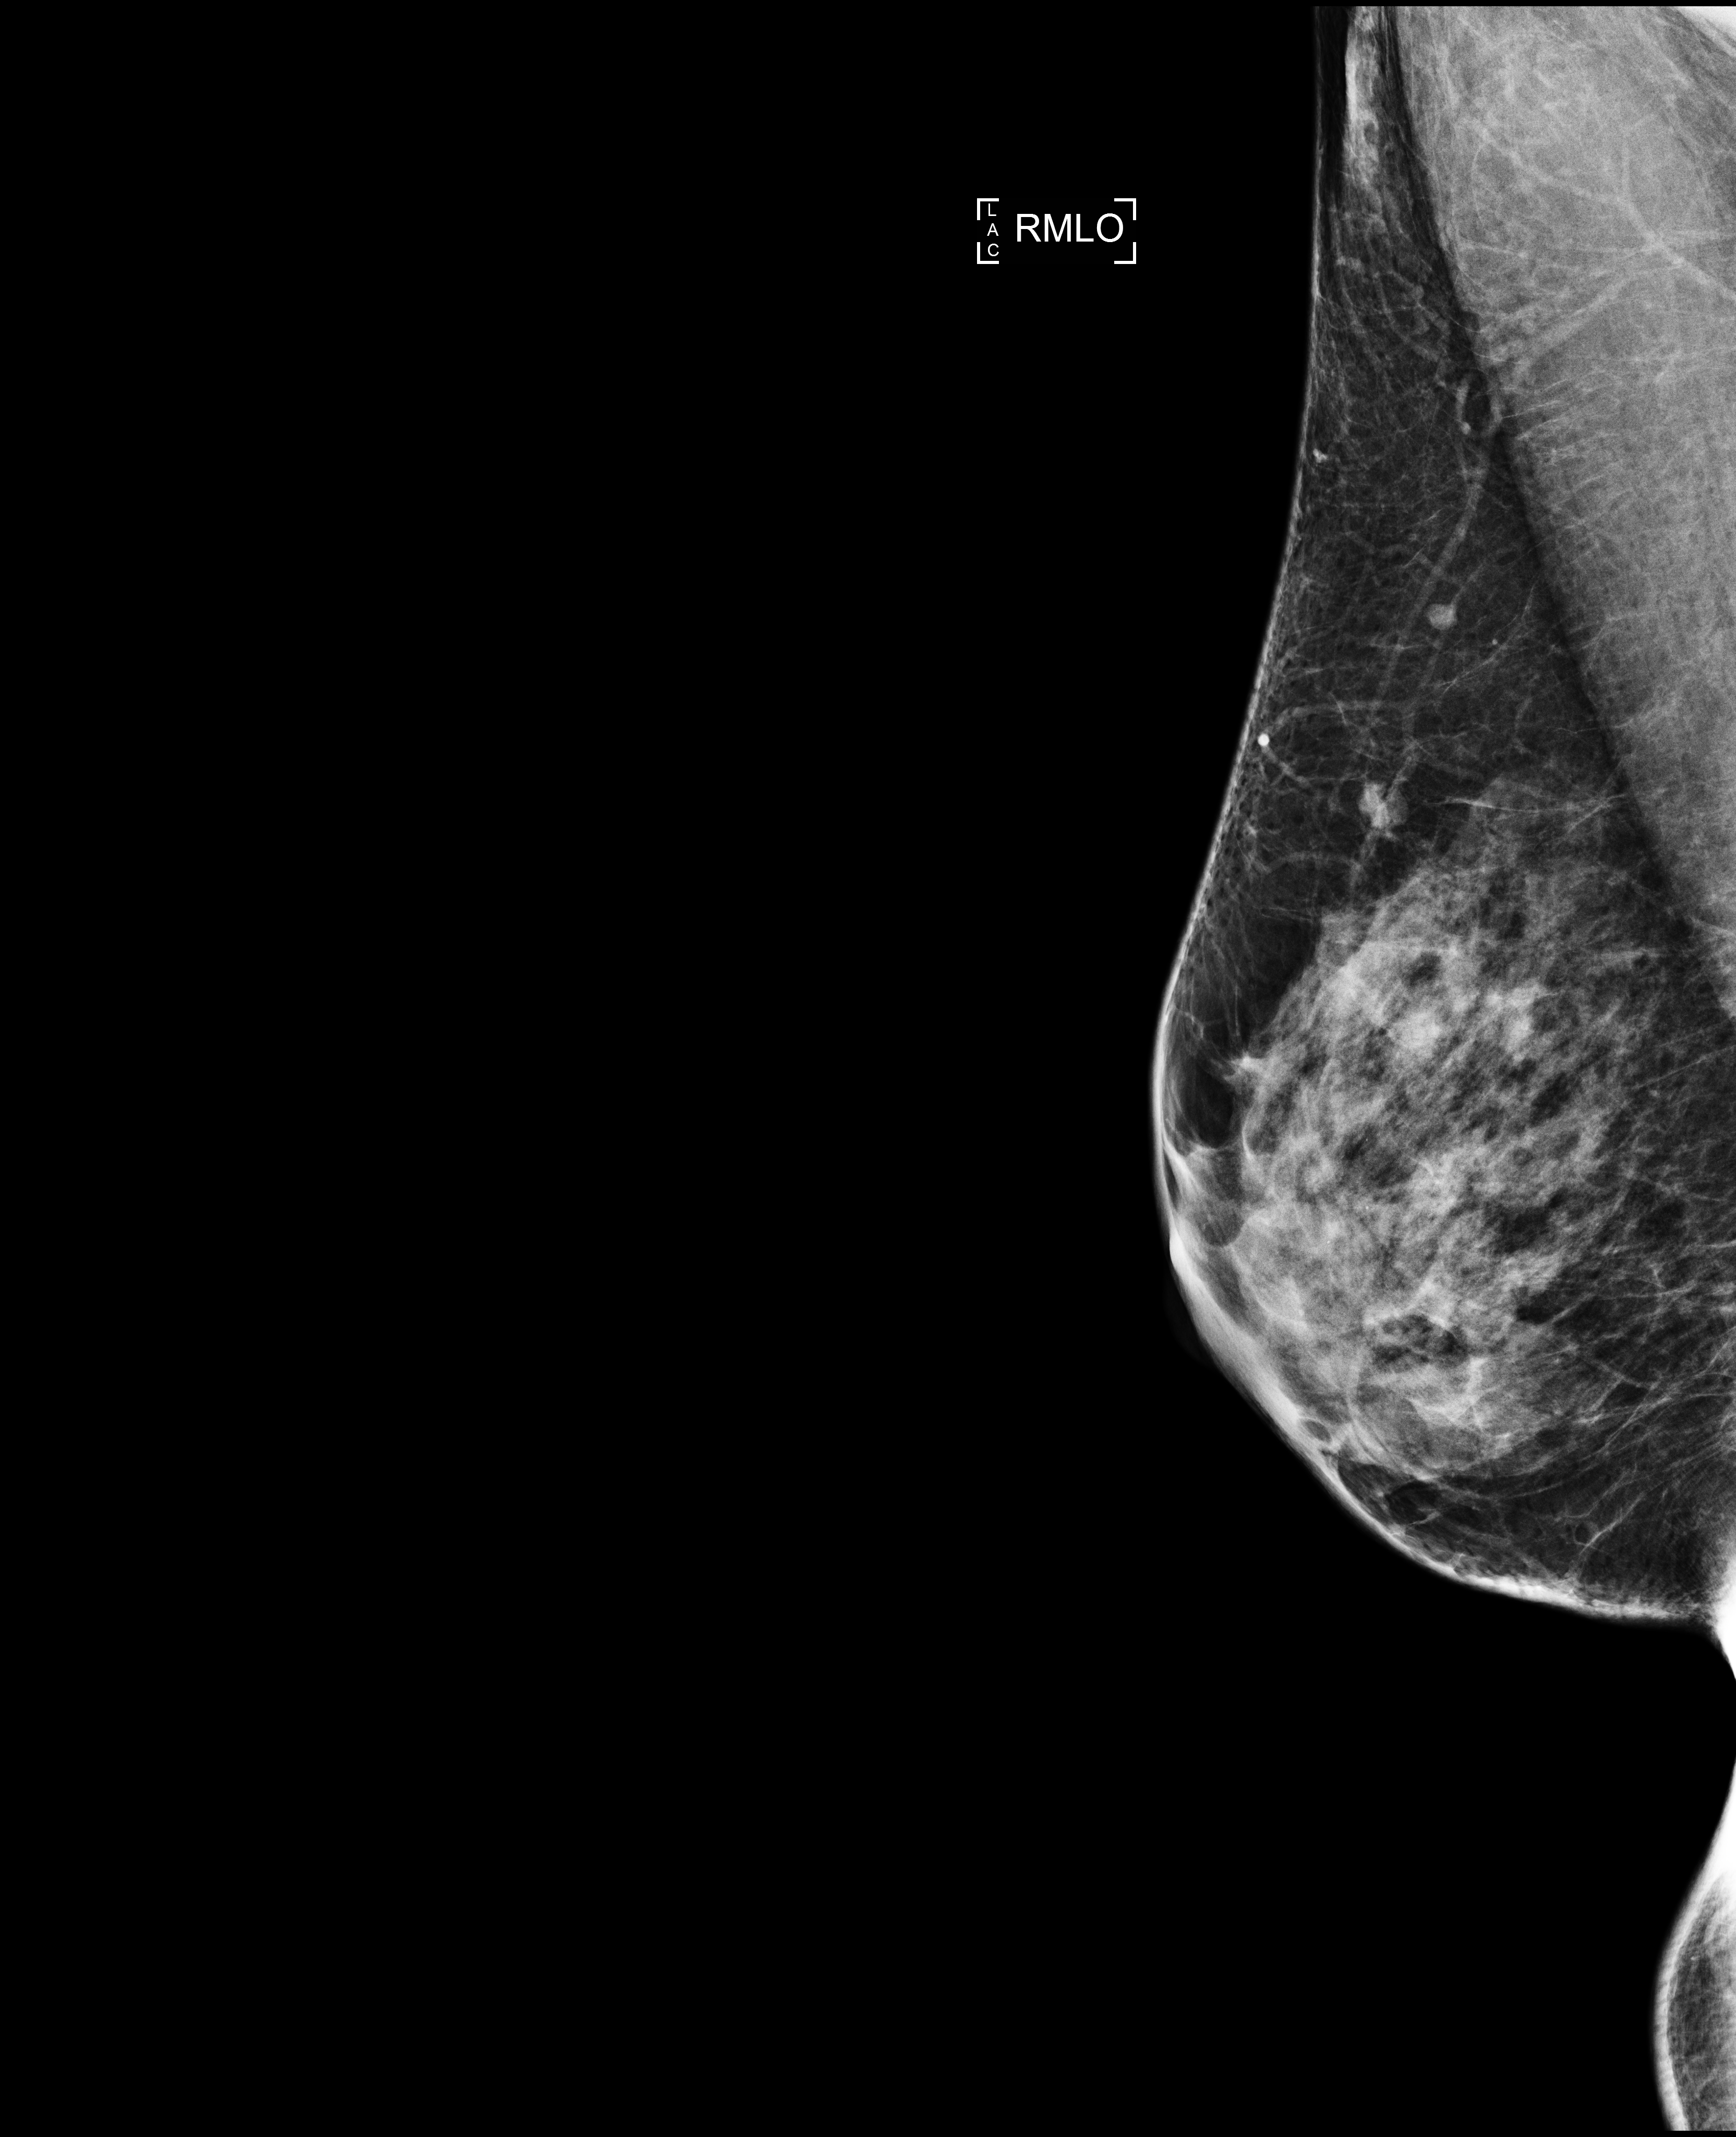
Screening examination; system: Selenia Dimensions. Patient aged 45 years (female).
Image type: full-field digital mammogram. Breast: right. Projection: MLO view.